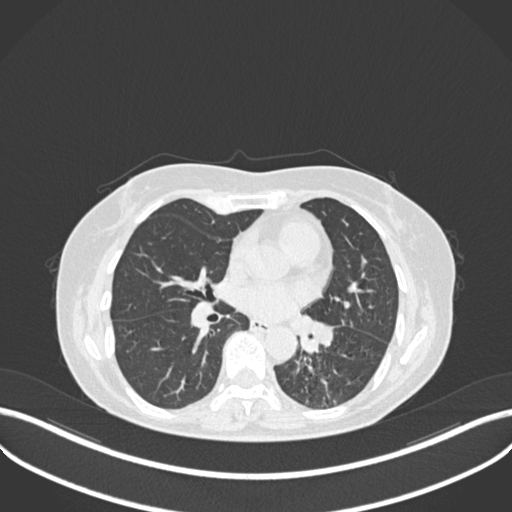
Chest CT, one axial slice; position 127 of 270 along the scan axis; reconstruction kernel B30f; 120 kVp; lung window (W 1500 / L -600 HU); 1 mm slice thickness; 512 × 512 image matrix, field of view 400 × 400 mm. Patient: female, 63 years. Case-level facts recorded for this patient, not image findings: clinical TNM (as recorded): T1b N0 M0; histopathological grade: G2-3.
Structures marked on this image (rectangle marked by the reading radiologist):
- lung tumour (recorded histology: adenocarcinoma): bounding box [x1, y1, x2, y2] px = [285, 308, 334, 357]